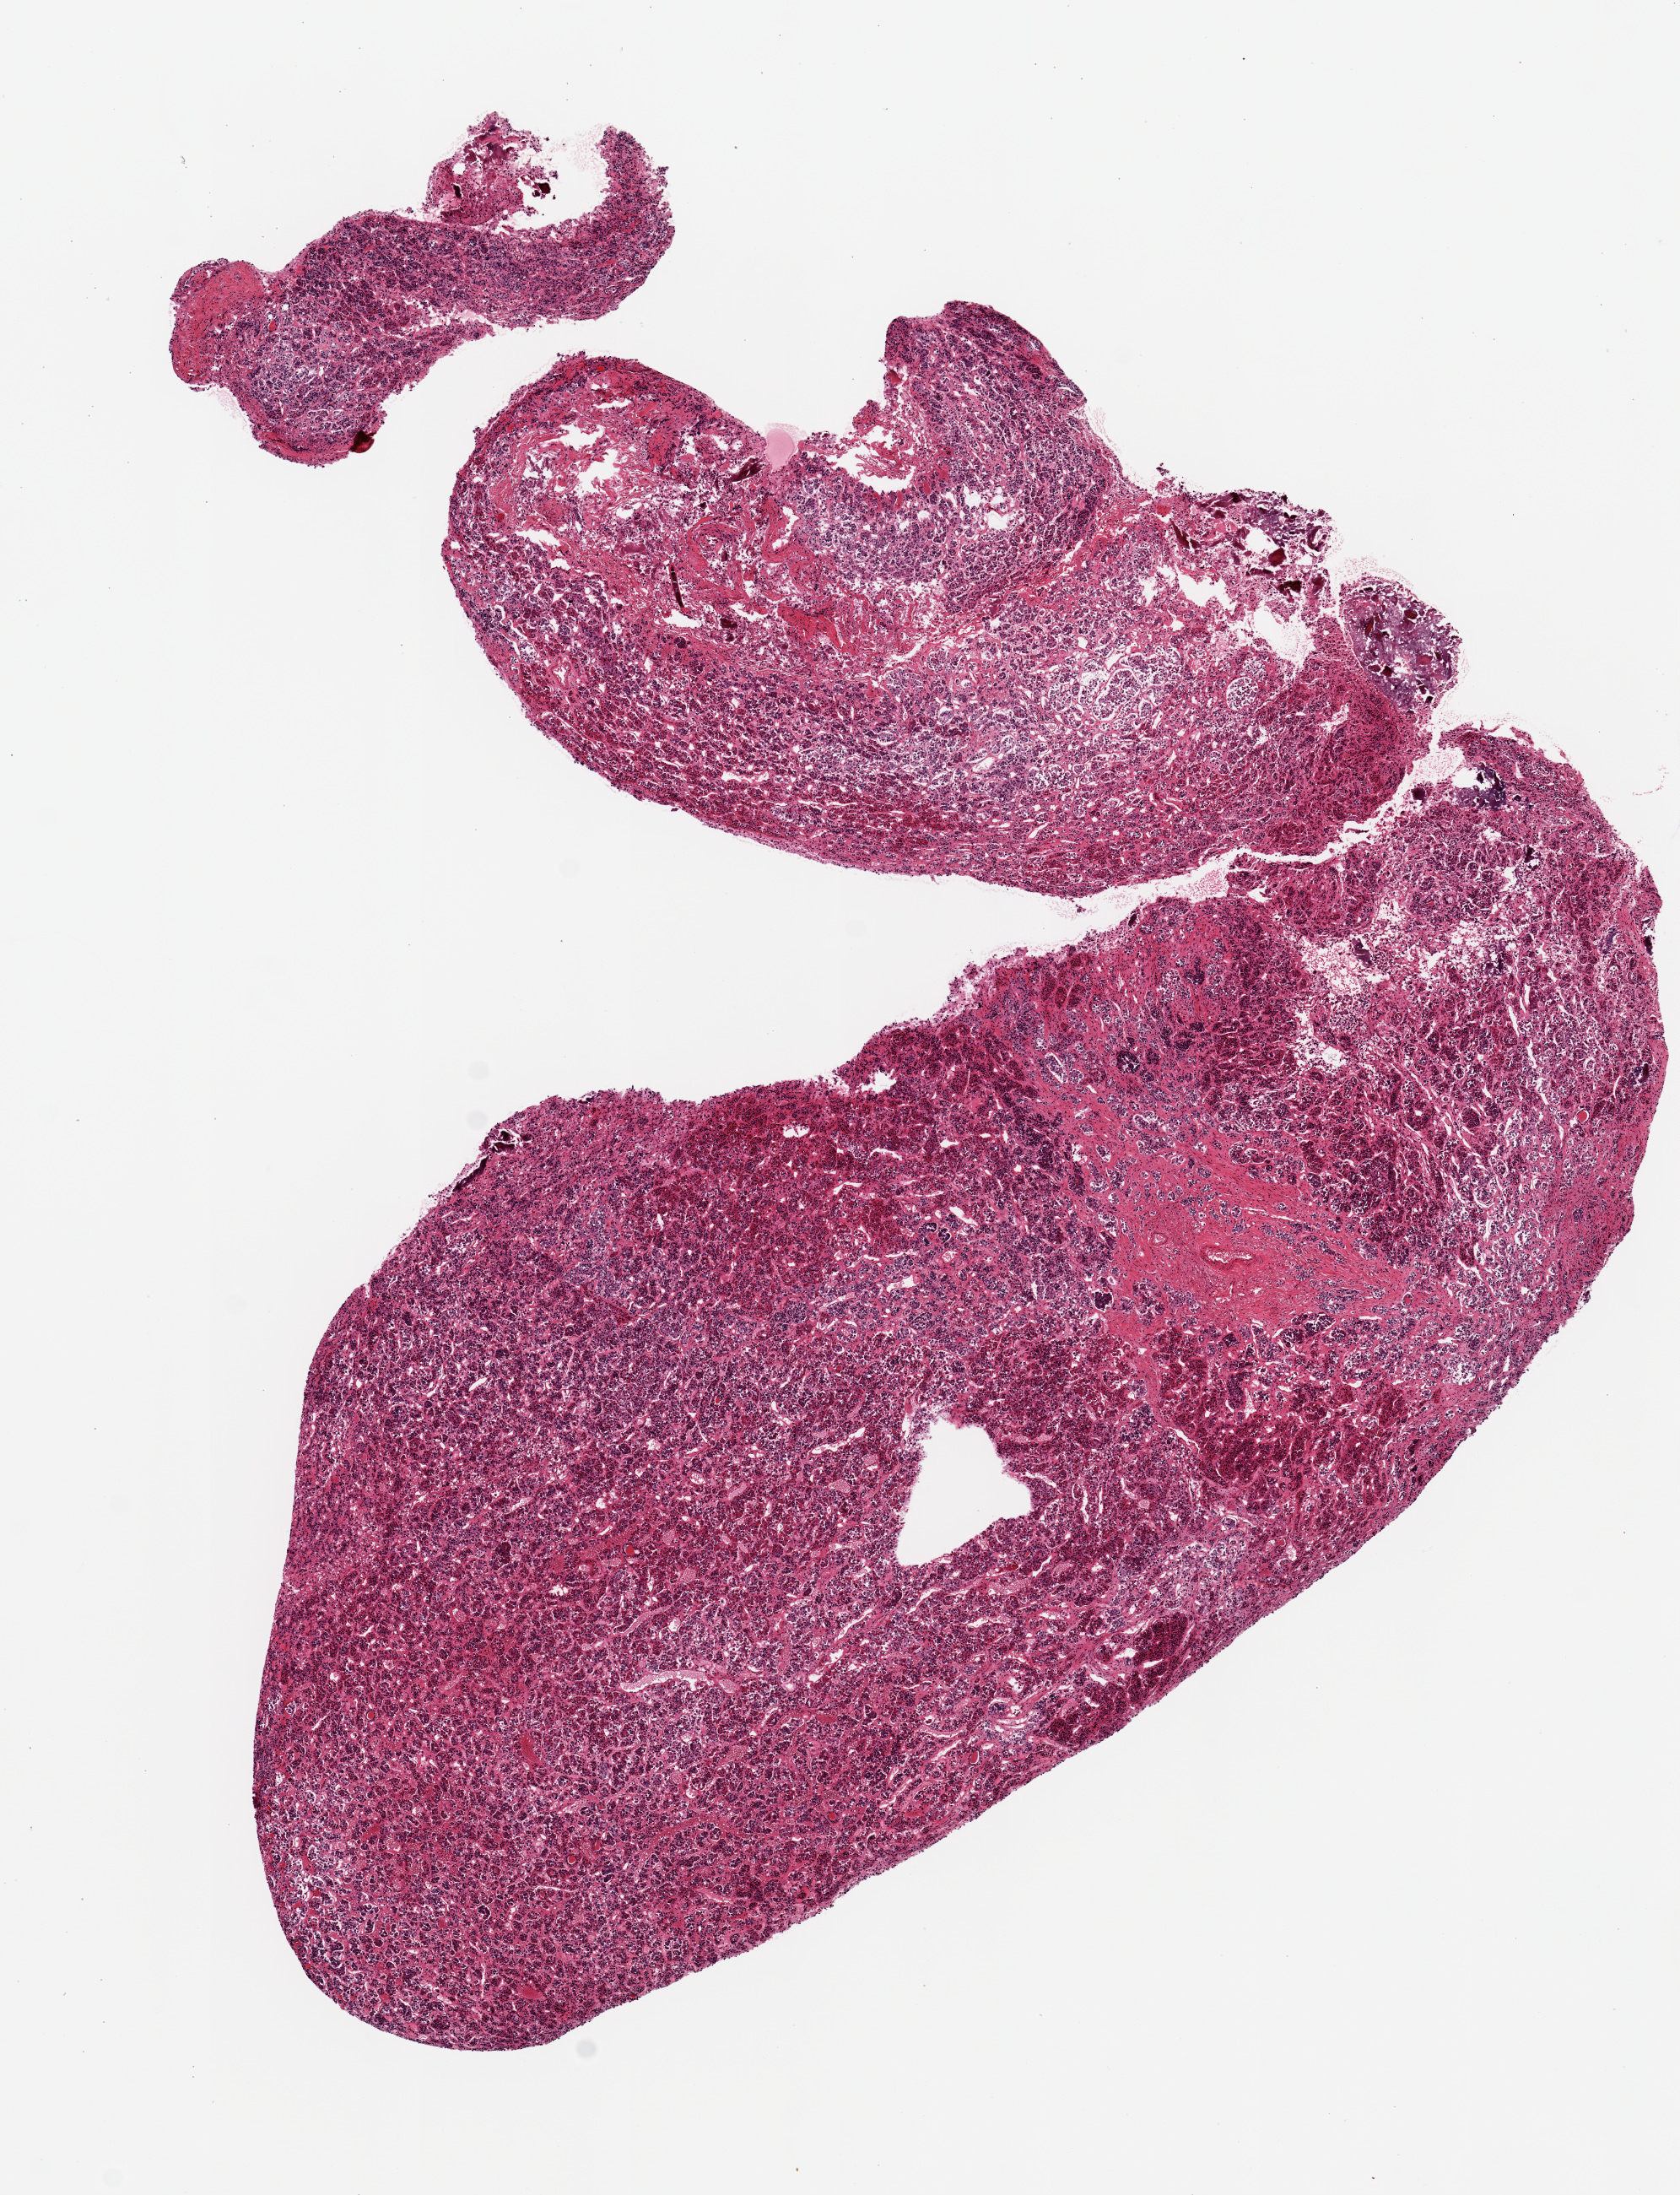
Digitized haematoxylin and eosin-stained section — a low-resolution overview of the entire scanned area, about 7.9 x 10.3 mm (acquisition: 20x scan). PAXgene-fixed, paraffin-embedded tissue. Sampled site (target tissue): pituitary. Tissue donor sample. Female donor.
Pathologist's review note for this sample: Fragmented ~9x7mm aliquot.